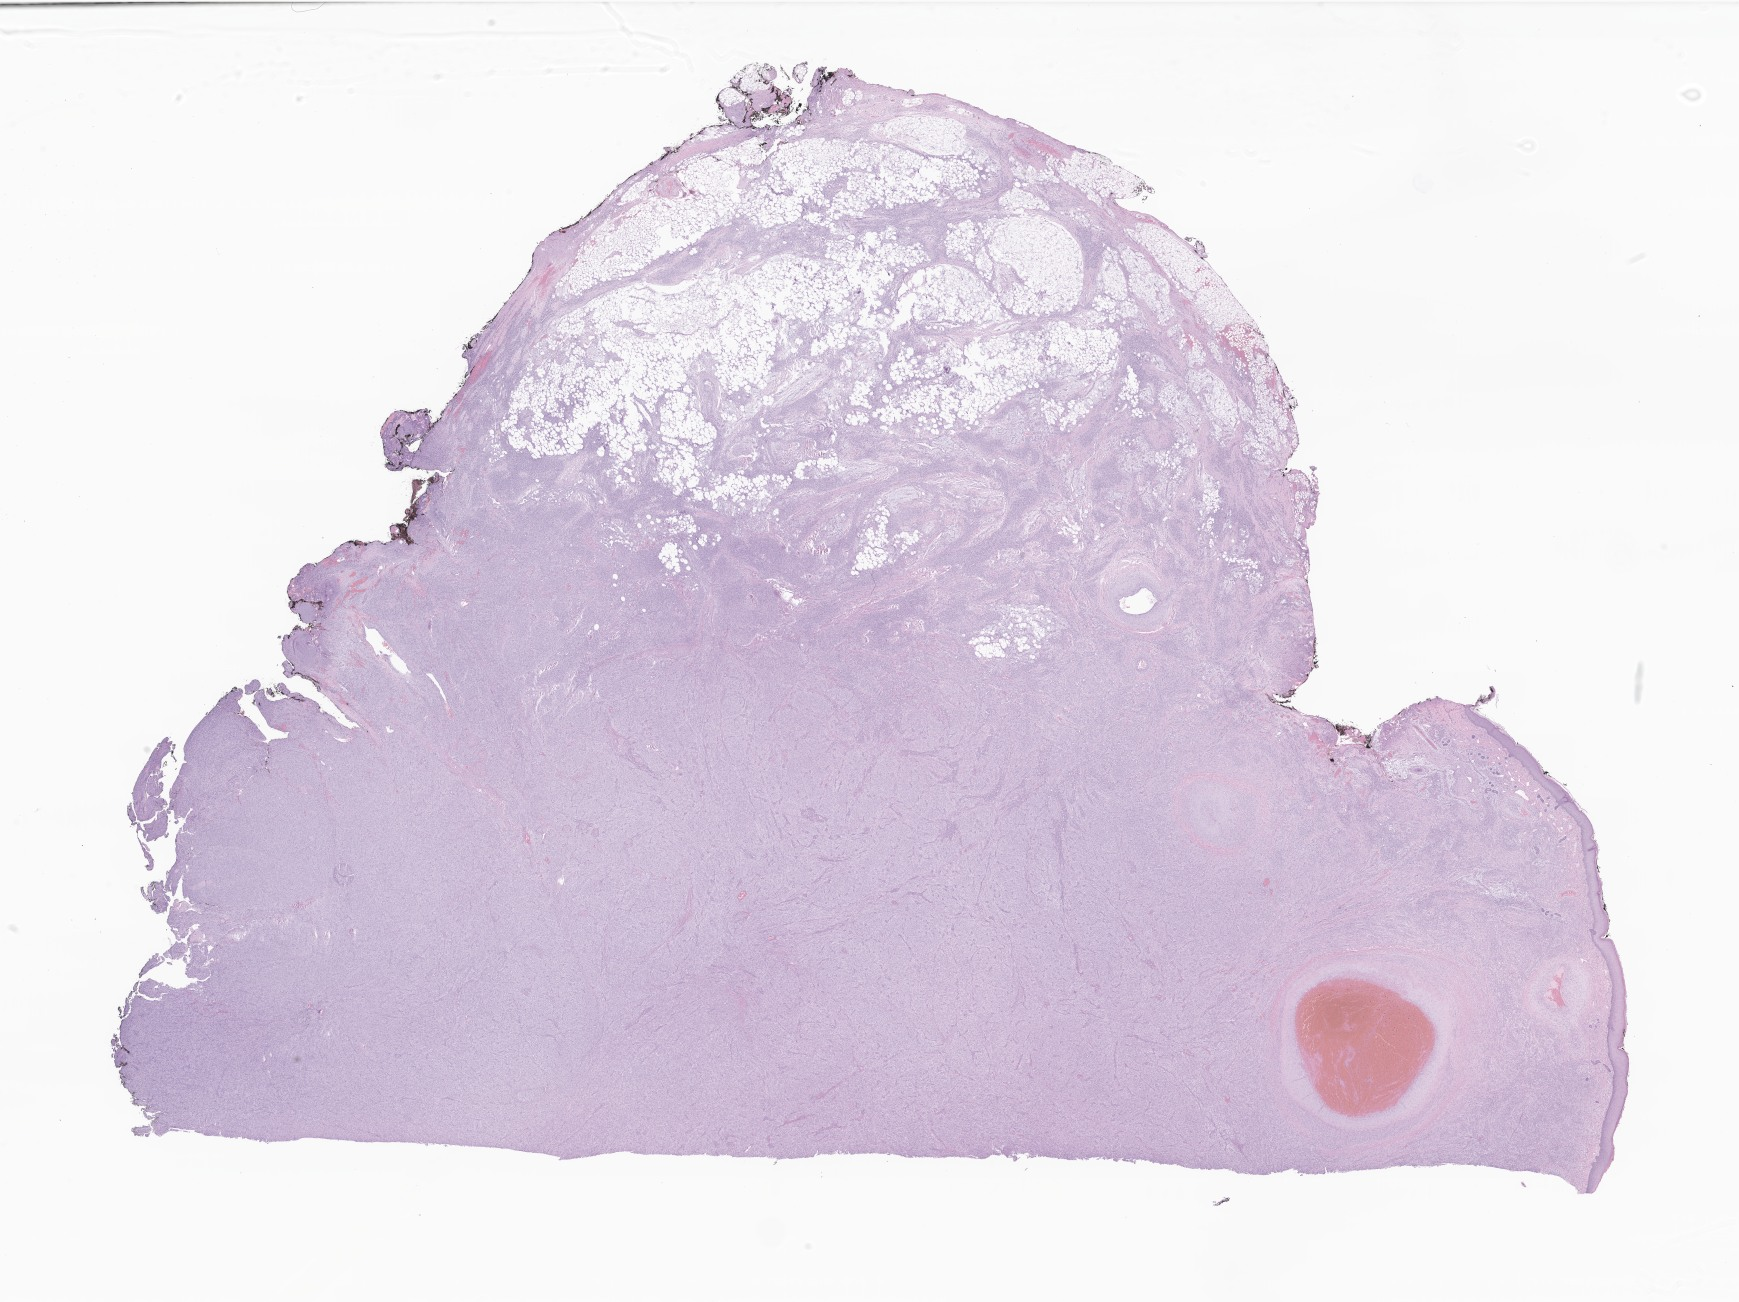
Haematoxylin and eosin whole-slide image of tumor tissue from the innominate bone and/or sacrum and/or coccyx — shown as a low-resolution overview of the whole scanned area (about 29.3 x 22.0 mm), FFPE section. Patient male; age 34 days.
Diagnosis (ICD-O-3 morphology term): Infantile fibrosarcoma.